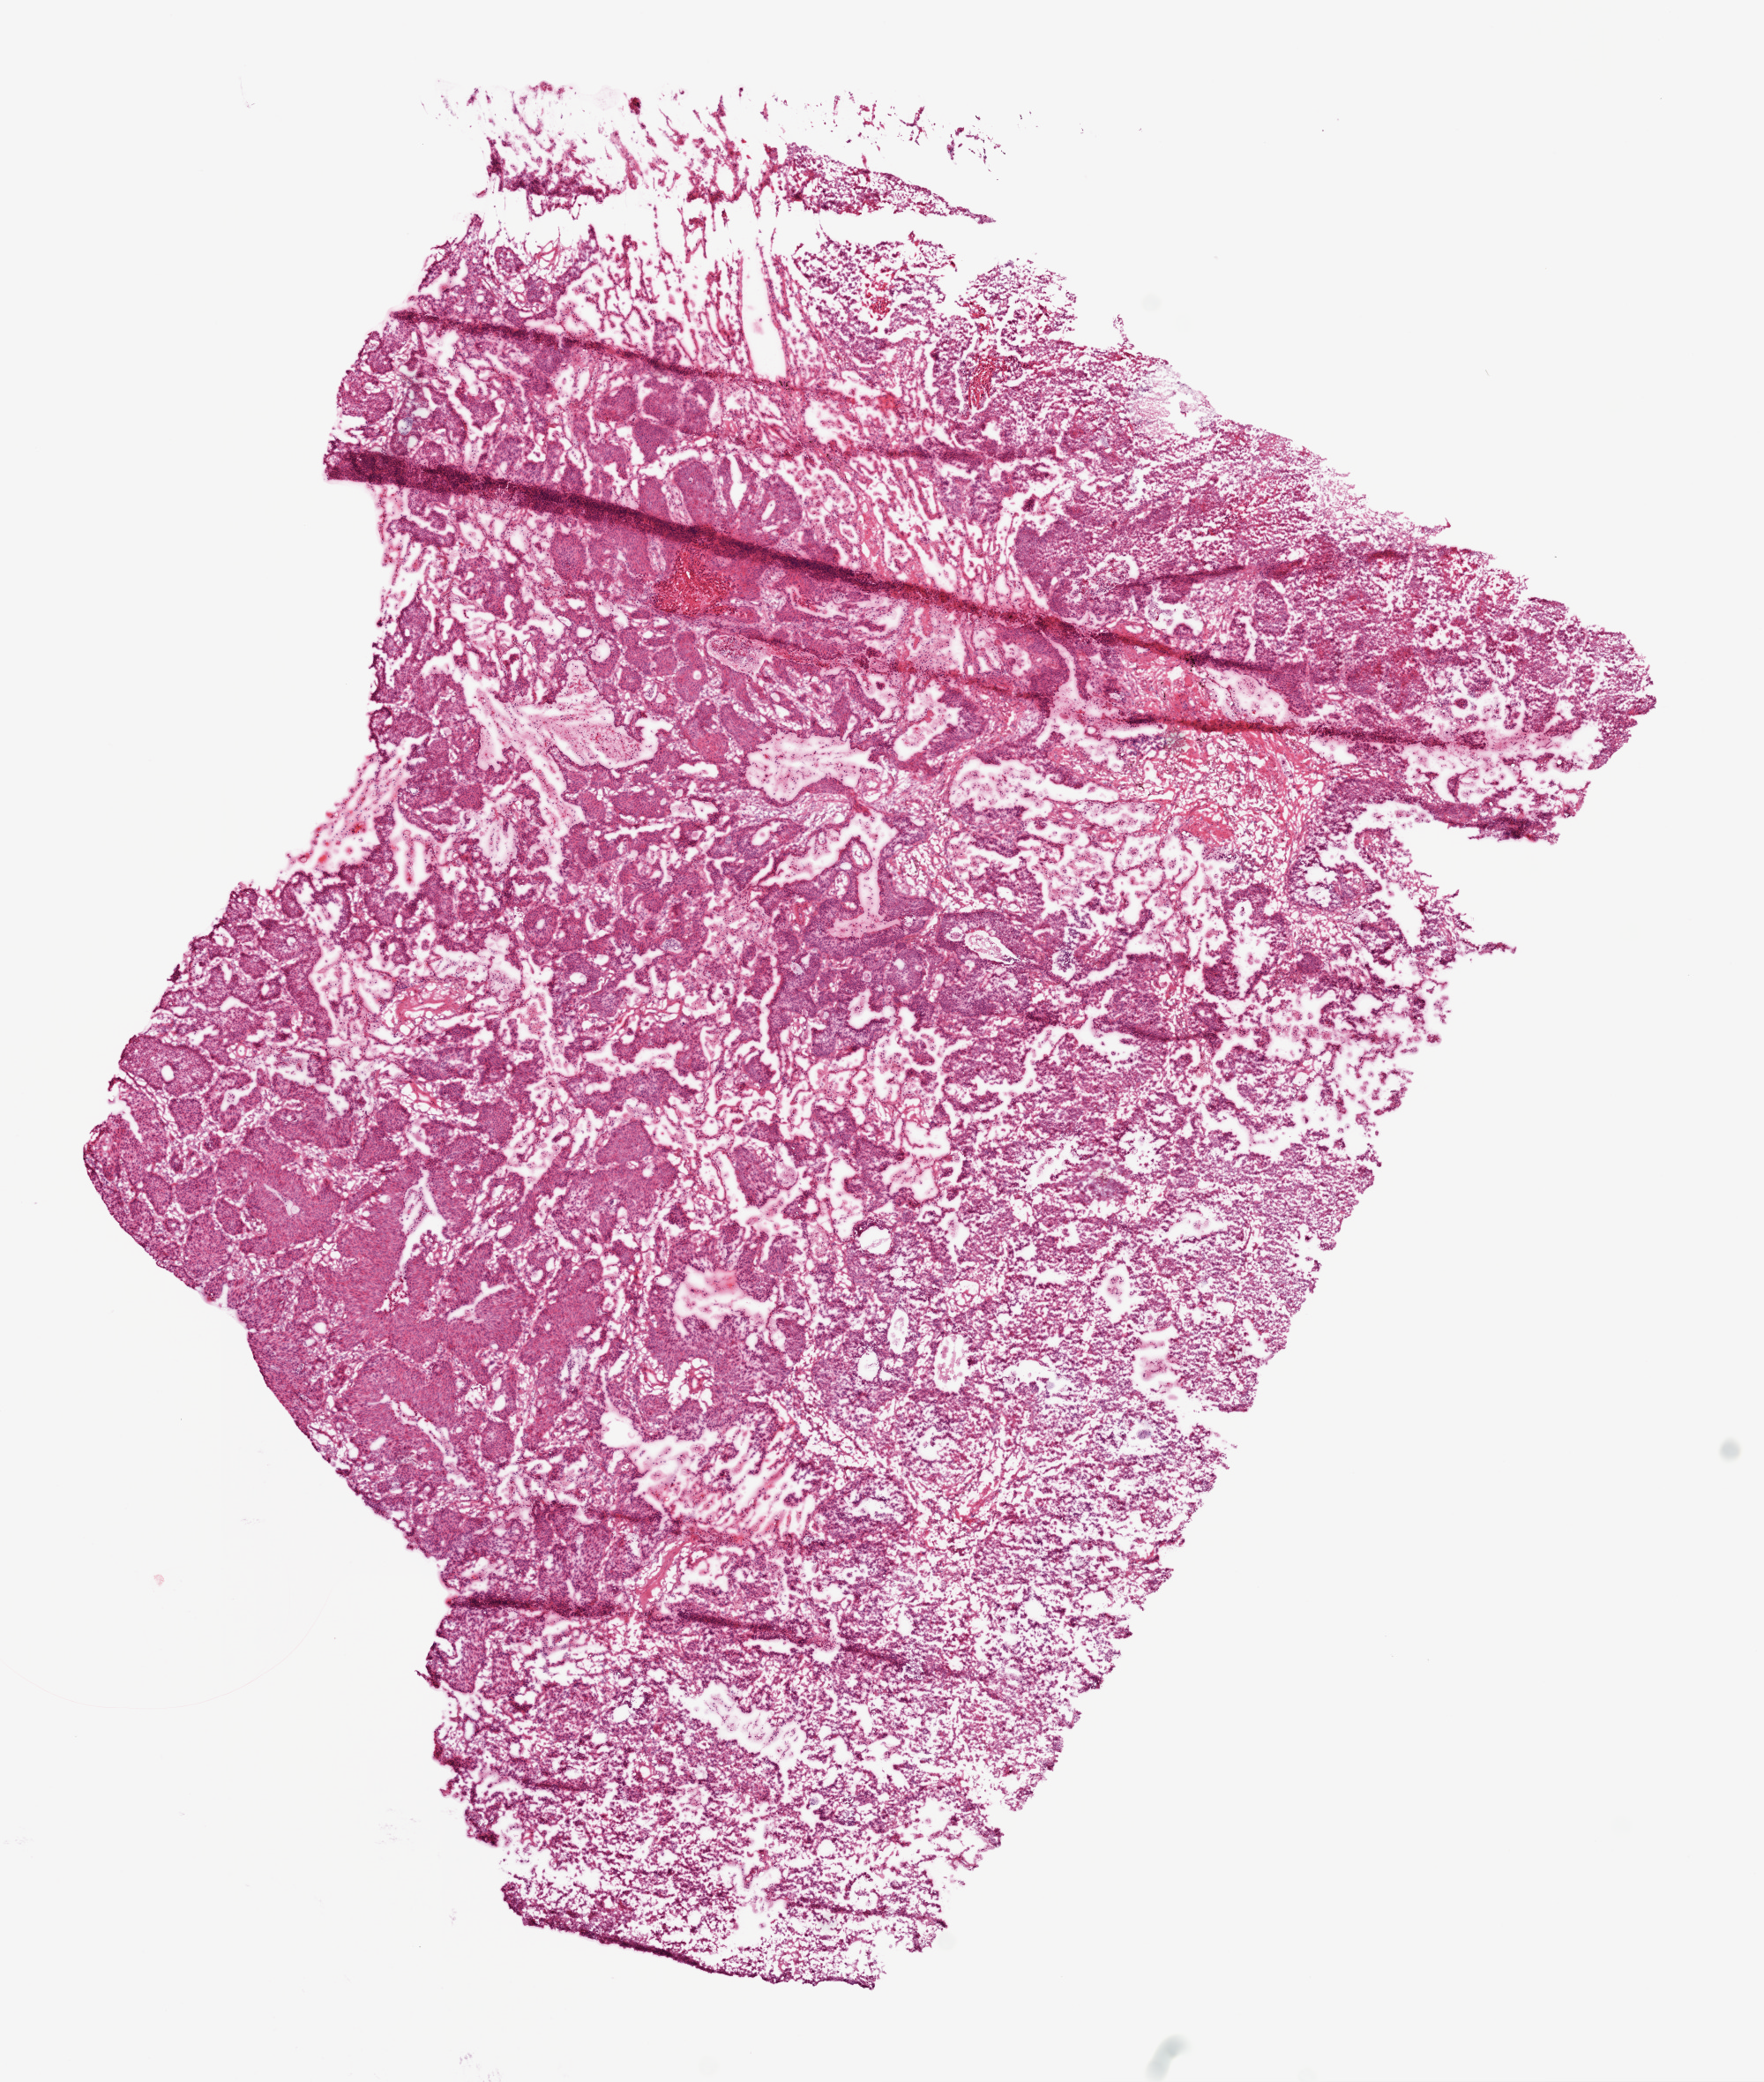
Whole-slide histology image, H&E-stained, shown as a low-resolution overview of the whole scanned area (about 8.0 x 9.5 mm), frozen section from the top of the tissue portion, sample: primary tumour, lung. Male, age 67 years at initial diagnosis. Pathologist review of this section (percent, as recorded): tumour cells 60%, tumour nuclei 80%, normal cells 10%, stromal cells 10%, necrosis 20%.
- histologic diagnosis: Squamous cell carcinoma, NOS (lower lobe, lung)
- laterality: right
- AJCC pathologic stage: IB